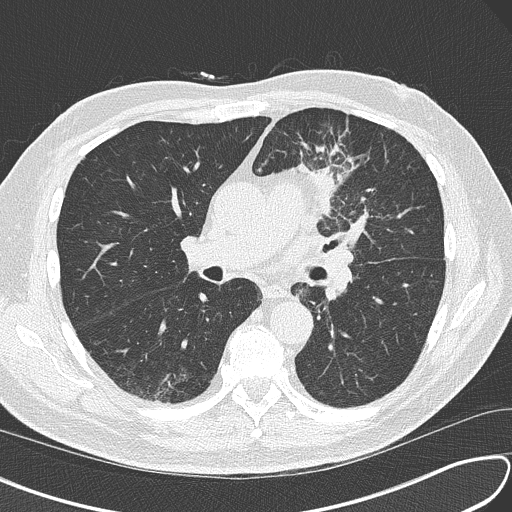
Chest CT (low-dose screening protocol), one axial image. Third annual screen. Lung window (W 1500 / L -600 HU). 2 mm slice thickness. Slice 71 of 156 in the series. 512 × 512 image matrix, field of view 340 × 340 mm. Male, age 67 years at enrolment.
Expert-annotated lung lesion, bounding box <292,153,392,241> (left, top, right, bottom; pixels). Screening reader's record for this exam (one nodule recorded; not confirmed to be the boxed lesion): non-calcified nodule or mass ≥4 mm, left upper lobe, 30 × 23 mm, soft tissue attenuation, pre-existing on the prior screen: no.